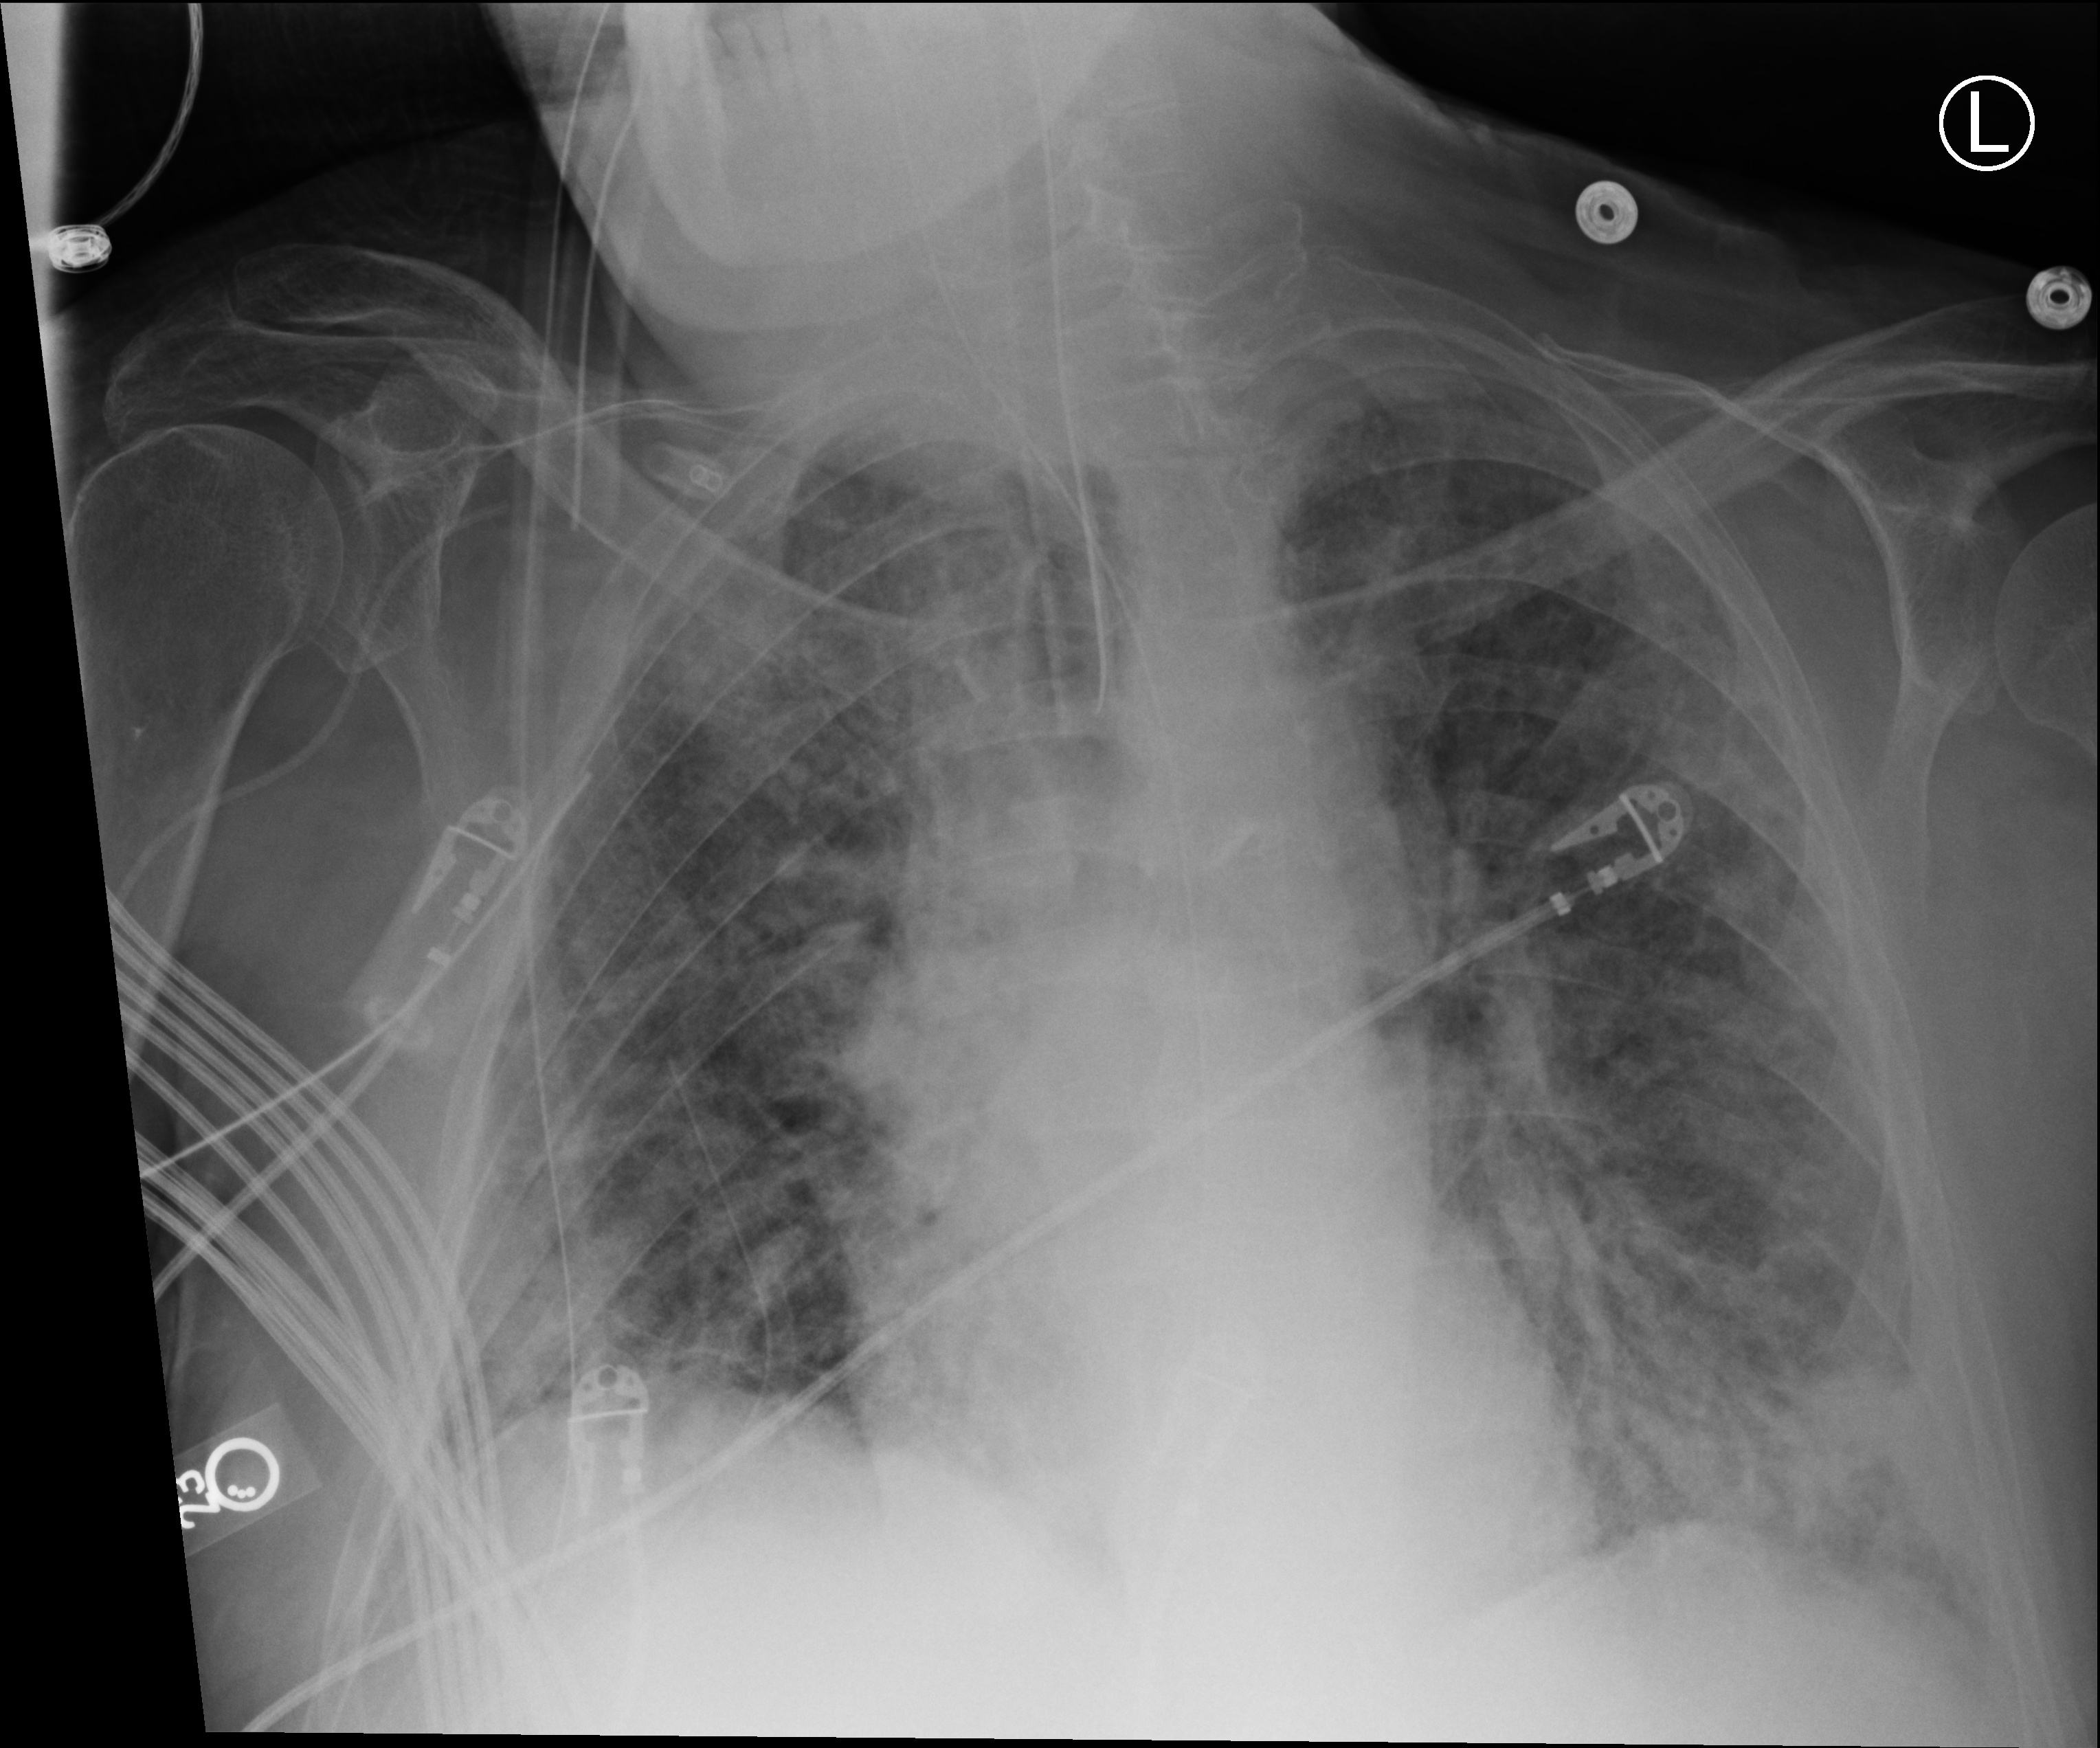
Chest X-ray (portable), anteroposterior (AP) projection. Male patient hospitalised with COVID-19, age 60–74 years.
Hospital-stay facts (about this admission, not read from this image; timing relative to this image not recorded): other chronic lung disease (admission record): no.